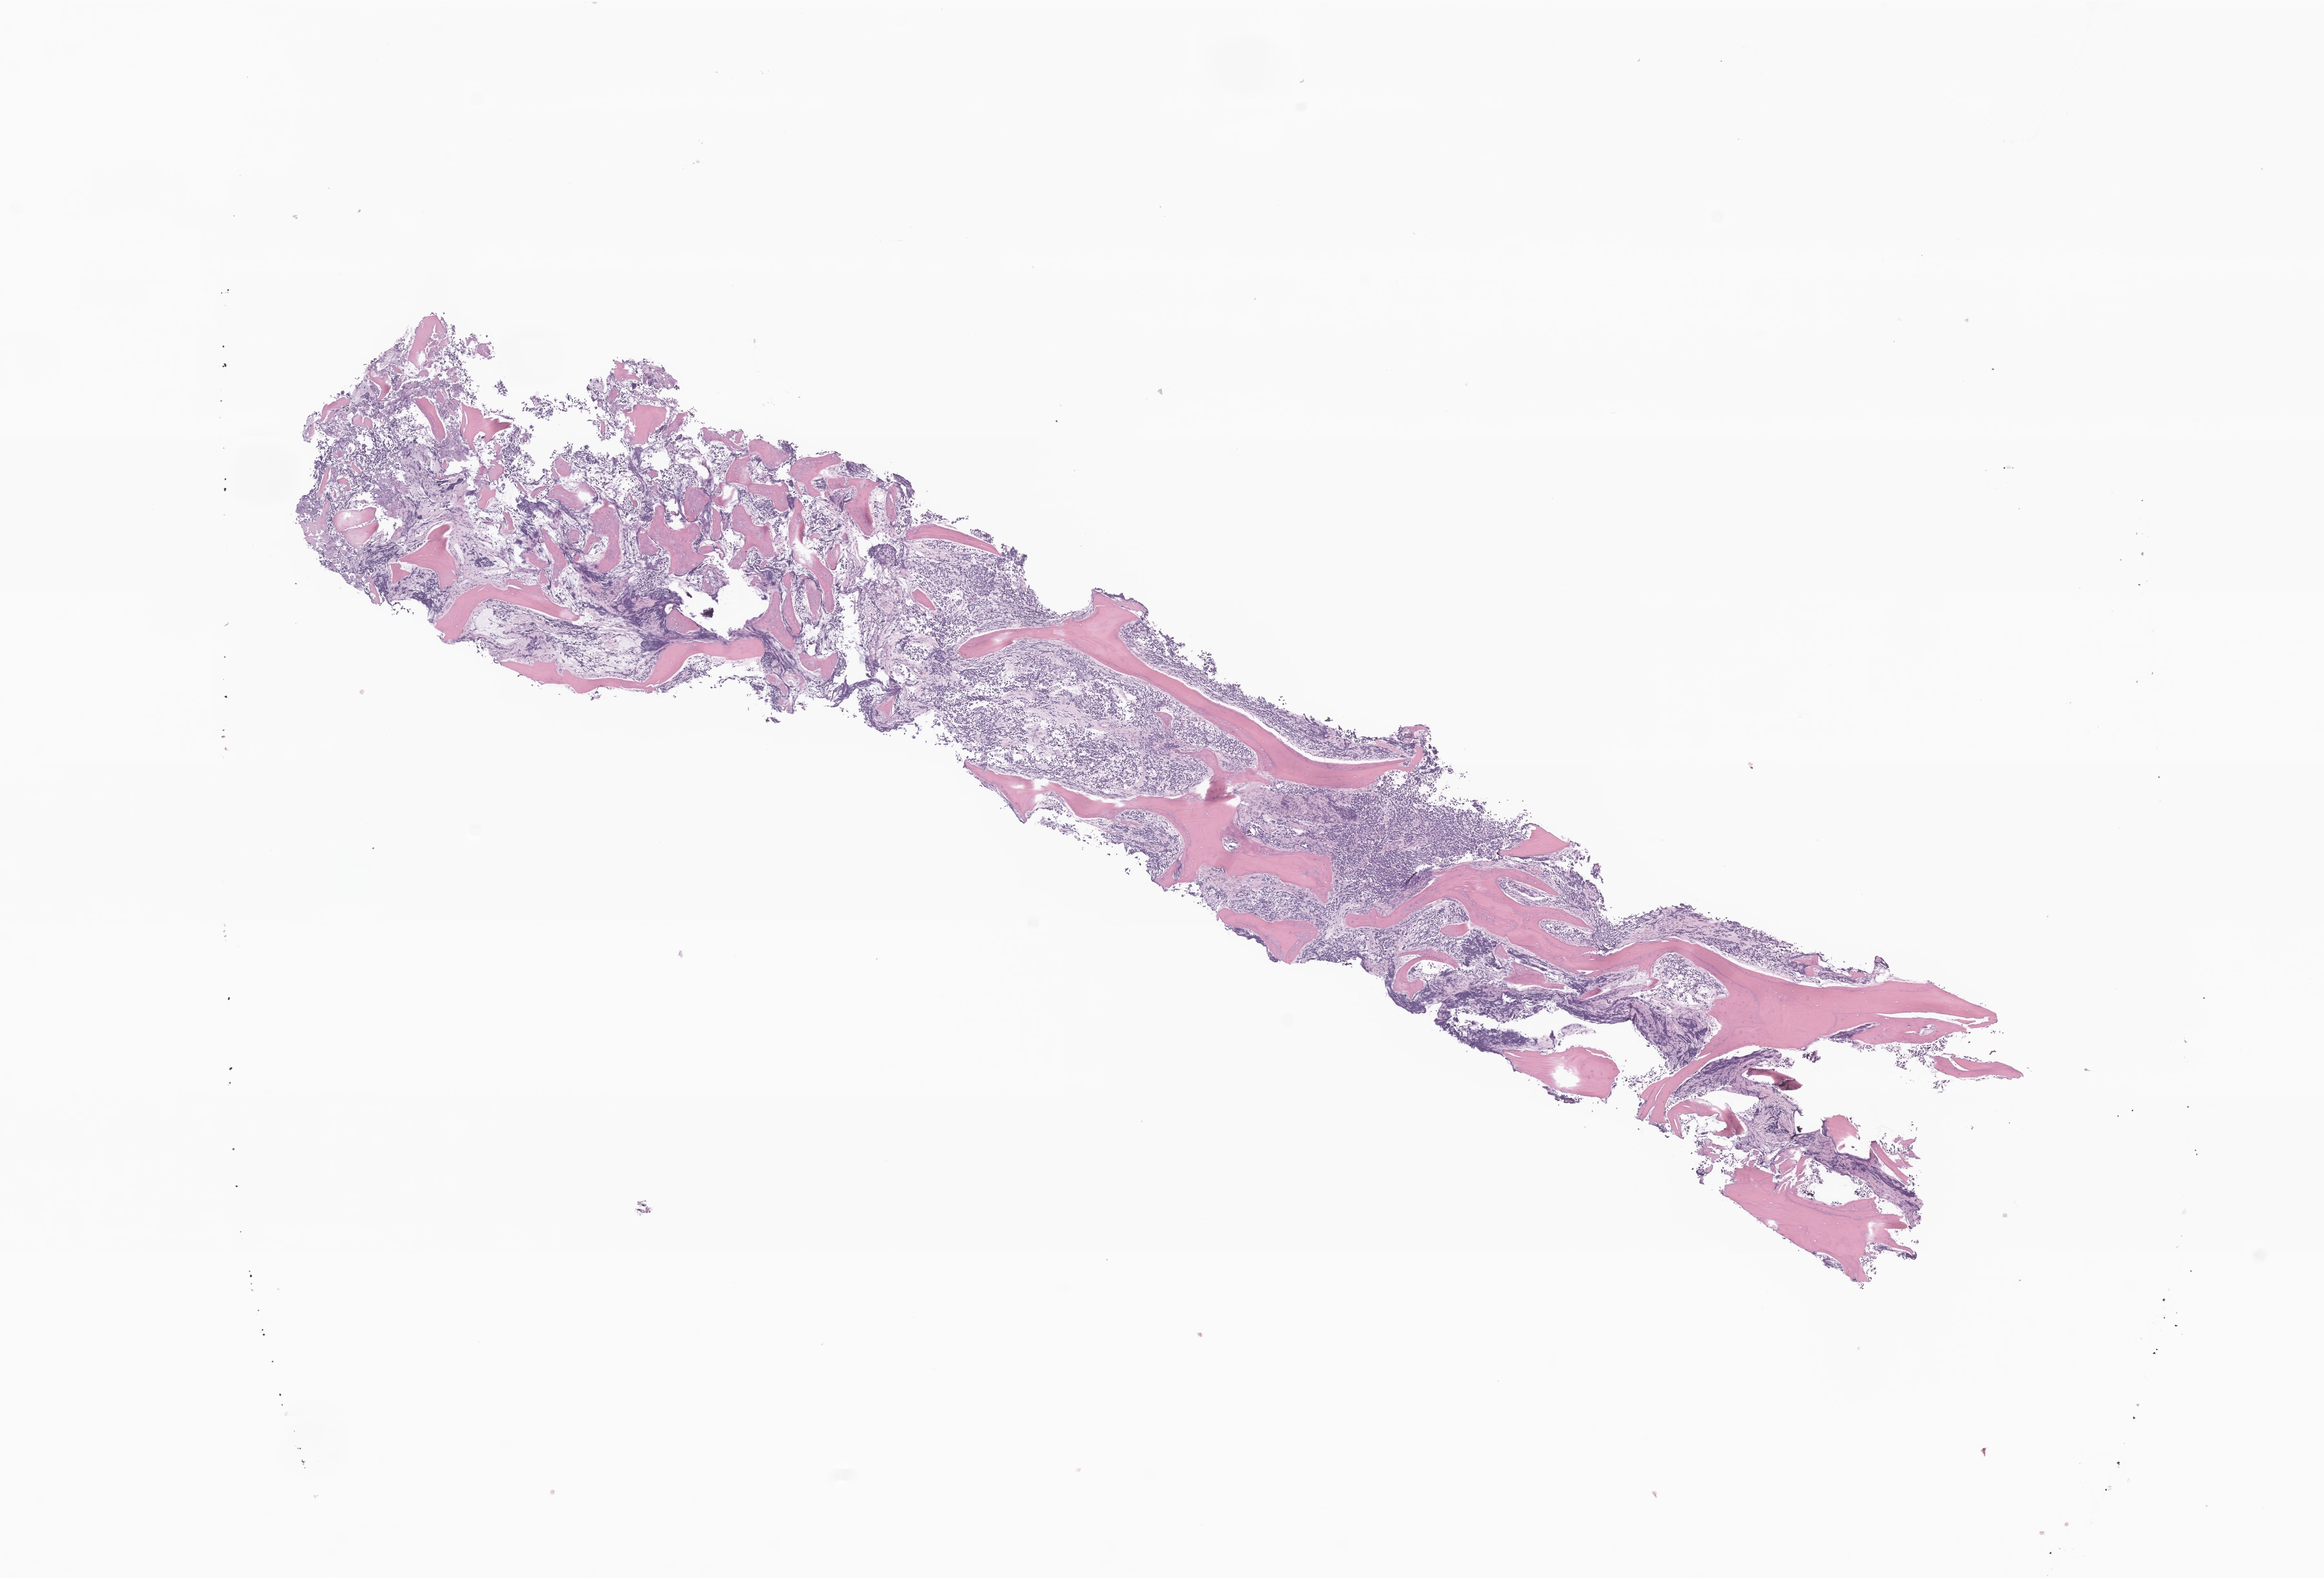
Haematoxylin and eosin whole-slide image of tumor tissue from the adrenal gland, low-resolution overview of the scanned area, about 15.2 x 10.3 mm; formalin-fixed, paraffin-embedded (FFPE) tissue. Patient: female, age 55 months (4 years 7 months).
Diagnosis: Neuroblastoma, NOS.